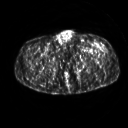
FDG PET of an extremity soft-tissue mass (from a PET/CT study), one axial slice; slice 262 of 267 in the series (ordered by position); 3.27 mm slice thickness; 128 × 128 image matrix, field of view 500 × 500 mm. Patient: male, 64 years. From the clinical record (not read from this slice): histological type: extraskeletal osteosarcoma; grade: high; site of the primary tumour: thigh.
Outlined on this slice (expert contour drawn on MRI and transferred to this co-registered scan by the dataset authors):
- gross tumour volume (mass): box from (x=102, y=45) to (x=105, y=49) px